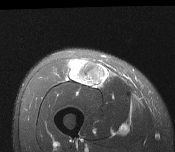
MRI of an extremity soft-tissue mass, one axial slice; T2-weighted fat-saturated; MR volume resampled by the dataset authors to the PET/CT grid (not the native acquisition matrix); 175 × 152 image matrix, field of view 171 × 148 mm. Male patient. From the clinical record (not read from this slice): histological type: pleiomorphic leiomyosarcoma; grade: intermediate; site of the primary tumour: right thigh.
Outlined on this slice (expert contour drawn on MRI and transferred to this co-registered scan by the dataset authors):
- gross tumour volume including surrounding oedema: bounding box <69,60,107,89> (left, top, right, bottom; pixels)